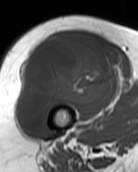
MRI of an extremity soft-tissue mass, one axial slice. MR volume resampled by the dataset authors to the PET/CT grid (not the native acquisition matrix). 3.27 mm slice thickness. 138 × 172 image matrix, field of view 135 × 168 mm. Female patient. From the clinical record (not read from this slice): histological type: pleiomorphic undifferentiated sarcoma; grade: high; site of the primary tumour: right quadricep.
Annotated regions visible in this slice (expert contour drawn on MRI and transferred to this co-registered scan by the dataset authors):
- gross tumour volume including surrounding oedema: bounding box <16,38,115,129> (left, top, right, bottom; pixels)
- gross tumour volume (mass): <16,38,115,129>